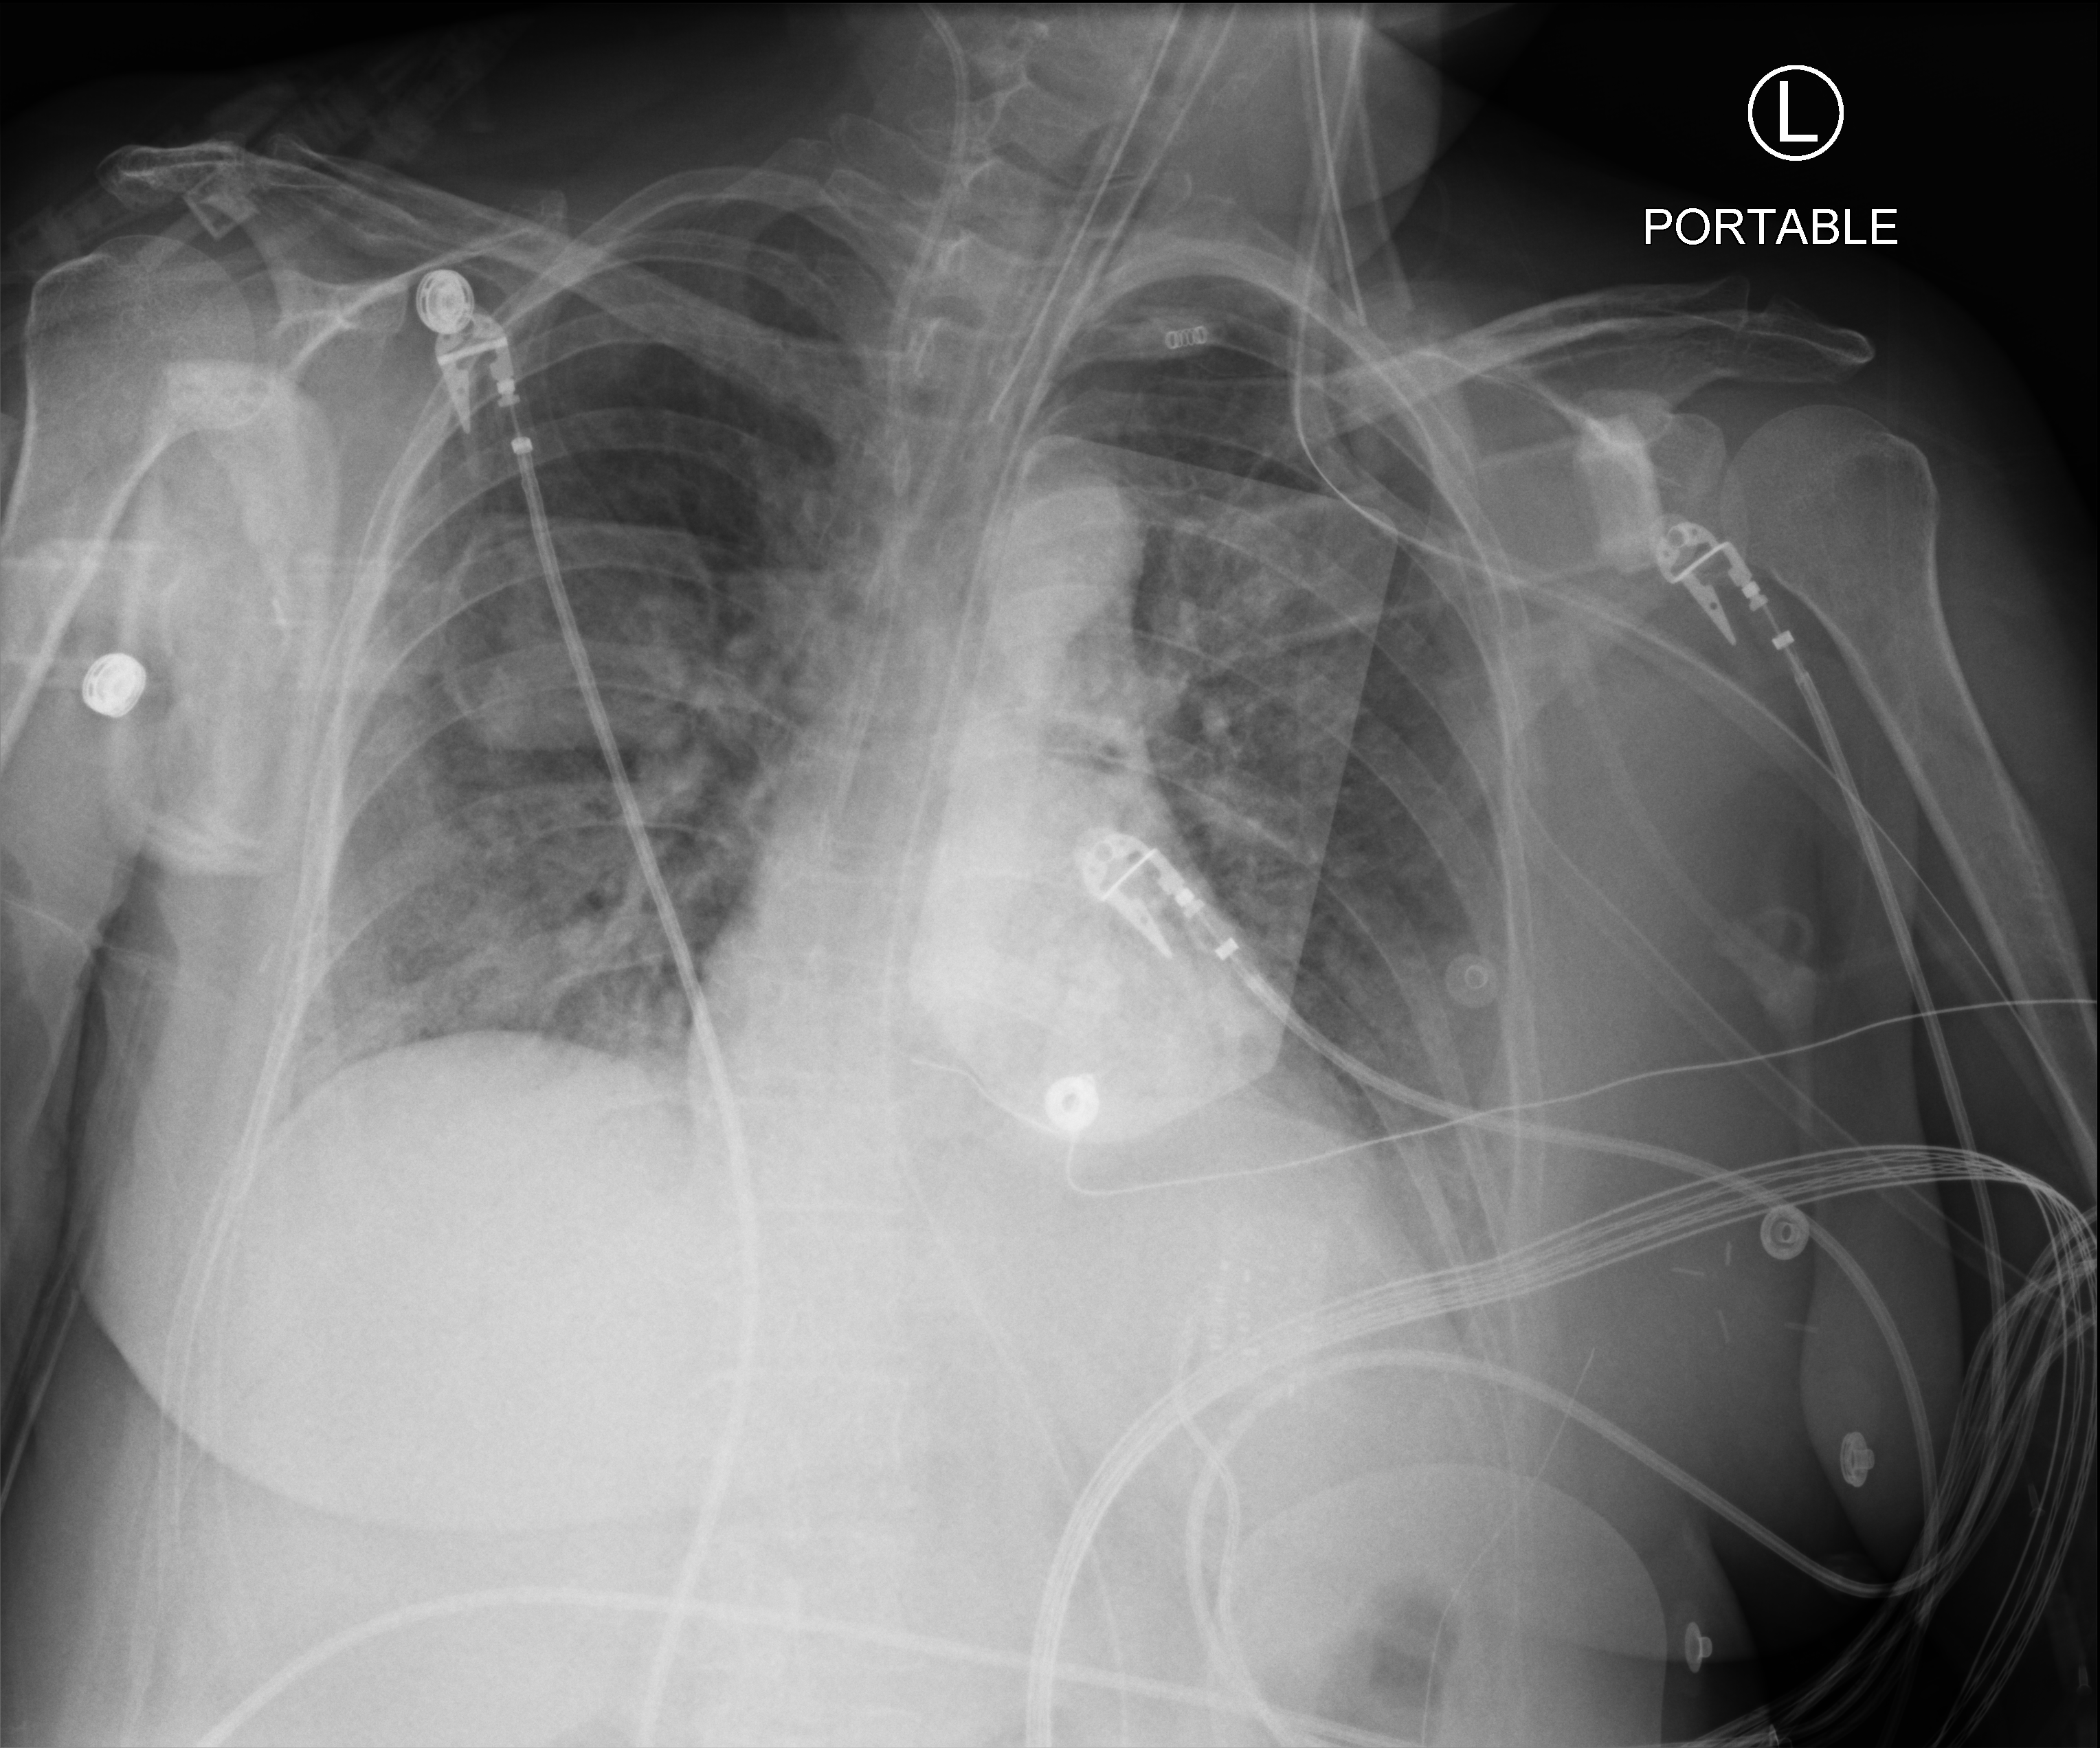
Portable chest radiograph; anteroposterior (AP) projection. Patient hospitalised with COVID-19; female, aged 18–59 years.
From the hospital-stay record, not from the radiograph (when in the stay this image was taken is not recorded):
- smoking status (admission record): never
- length of hospital stay: 21 days
- admitted to intensive care during this hospital stay: no